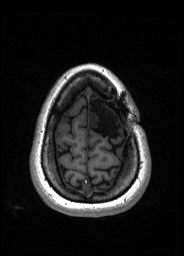
Pre-operative brain MRI before brain-tumour surgery, one axial slice. Slice 36 of 176 in the series (ordered by position). T1-weighted post-contrast. 1 mm slice thickness. 184 × 256 image matrix. Case-level facts recorded for this patient, not image findings: histopathology: Oligodendroglioma; WHO grade: 2; IDH mutation: yes.
Structures marked on this image (outlined manually by an expert reader):
- tumour: bounding box <88,111,99,127> (left, top, right, bottom; pixels)